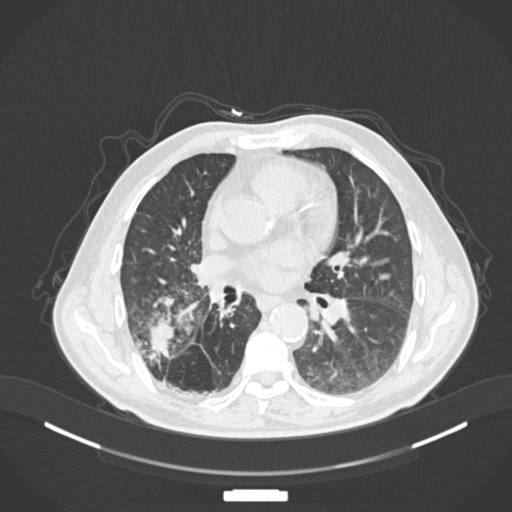
Chest CT, one axial slice; slice 81 of 201 in the series (ordered by position); reconstruction kernel B30f; 120 kVp; lung window (W 1500 / L -600 HU); 1 mm slice thickness; 512 × 512 image matrix, field of view 400 × 400 mm. Male patient, age 72 years. From the clinical record (not read from this slice): clinical TNM (as recorded): T3 N2 M0.
Annotated regions visible in this slice (rectangle marked by the reading radiologist):
- lung tumour (recorded histology: adenocarcinoma): bounding box [x1, y1, x2, y2] px = [141, 311, 179, 364]